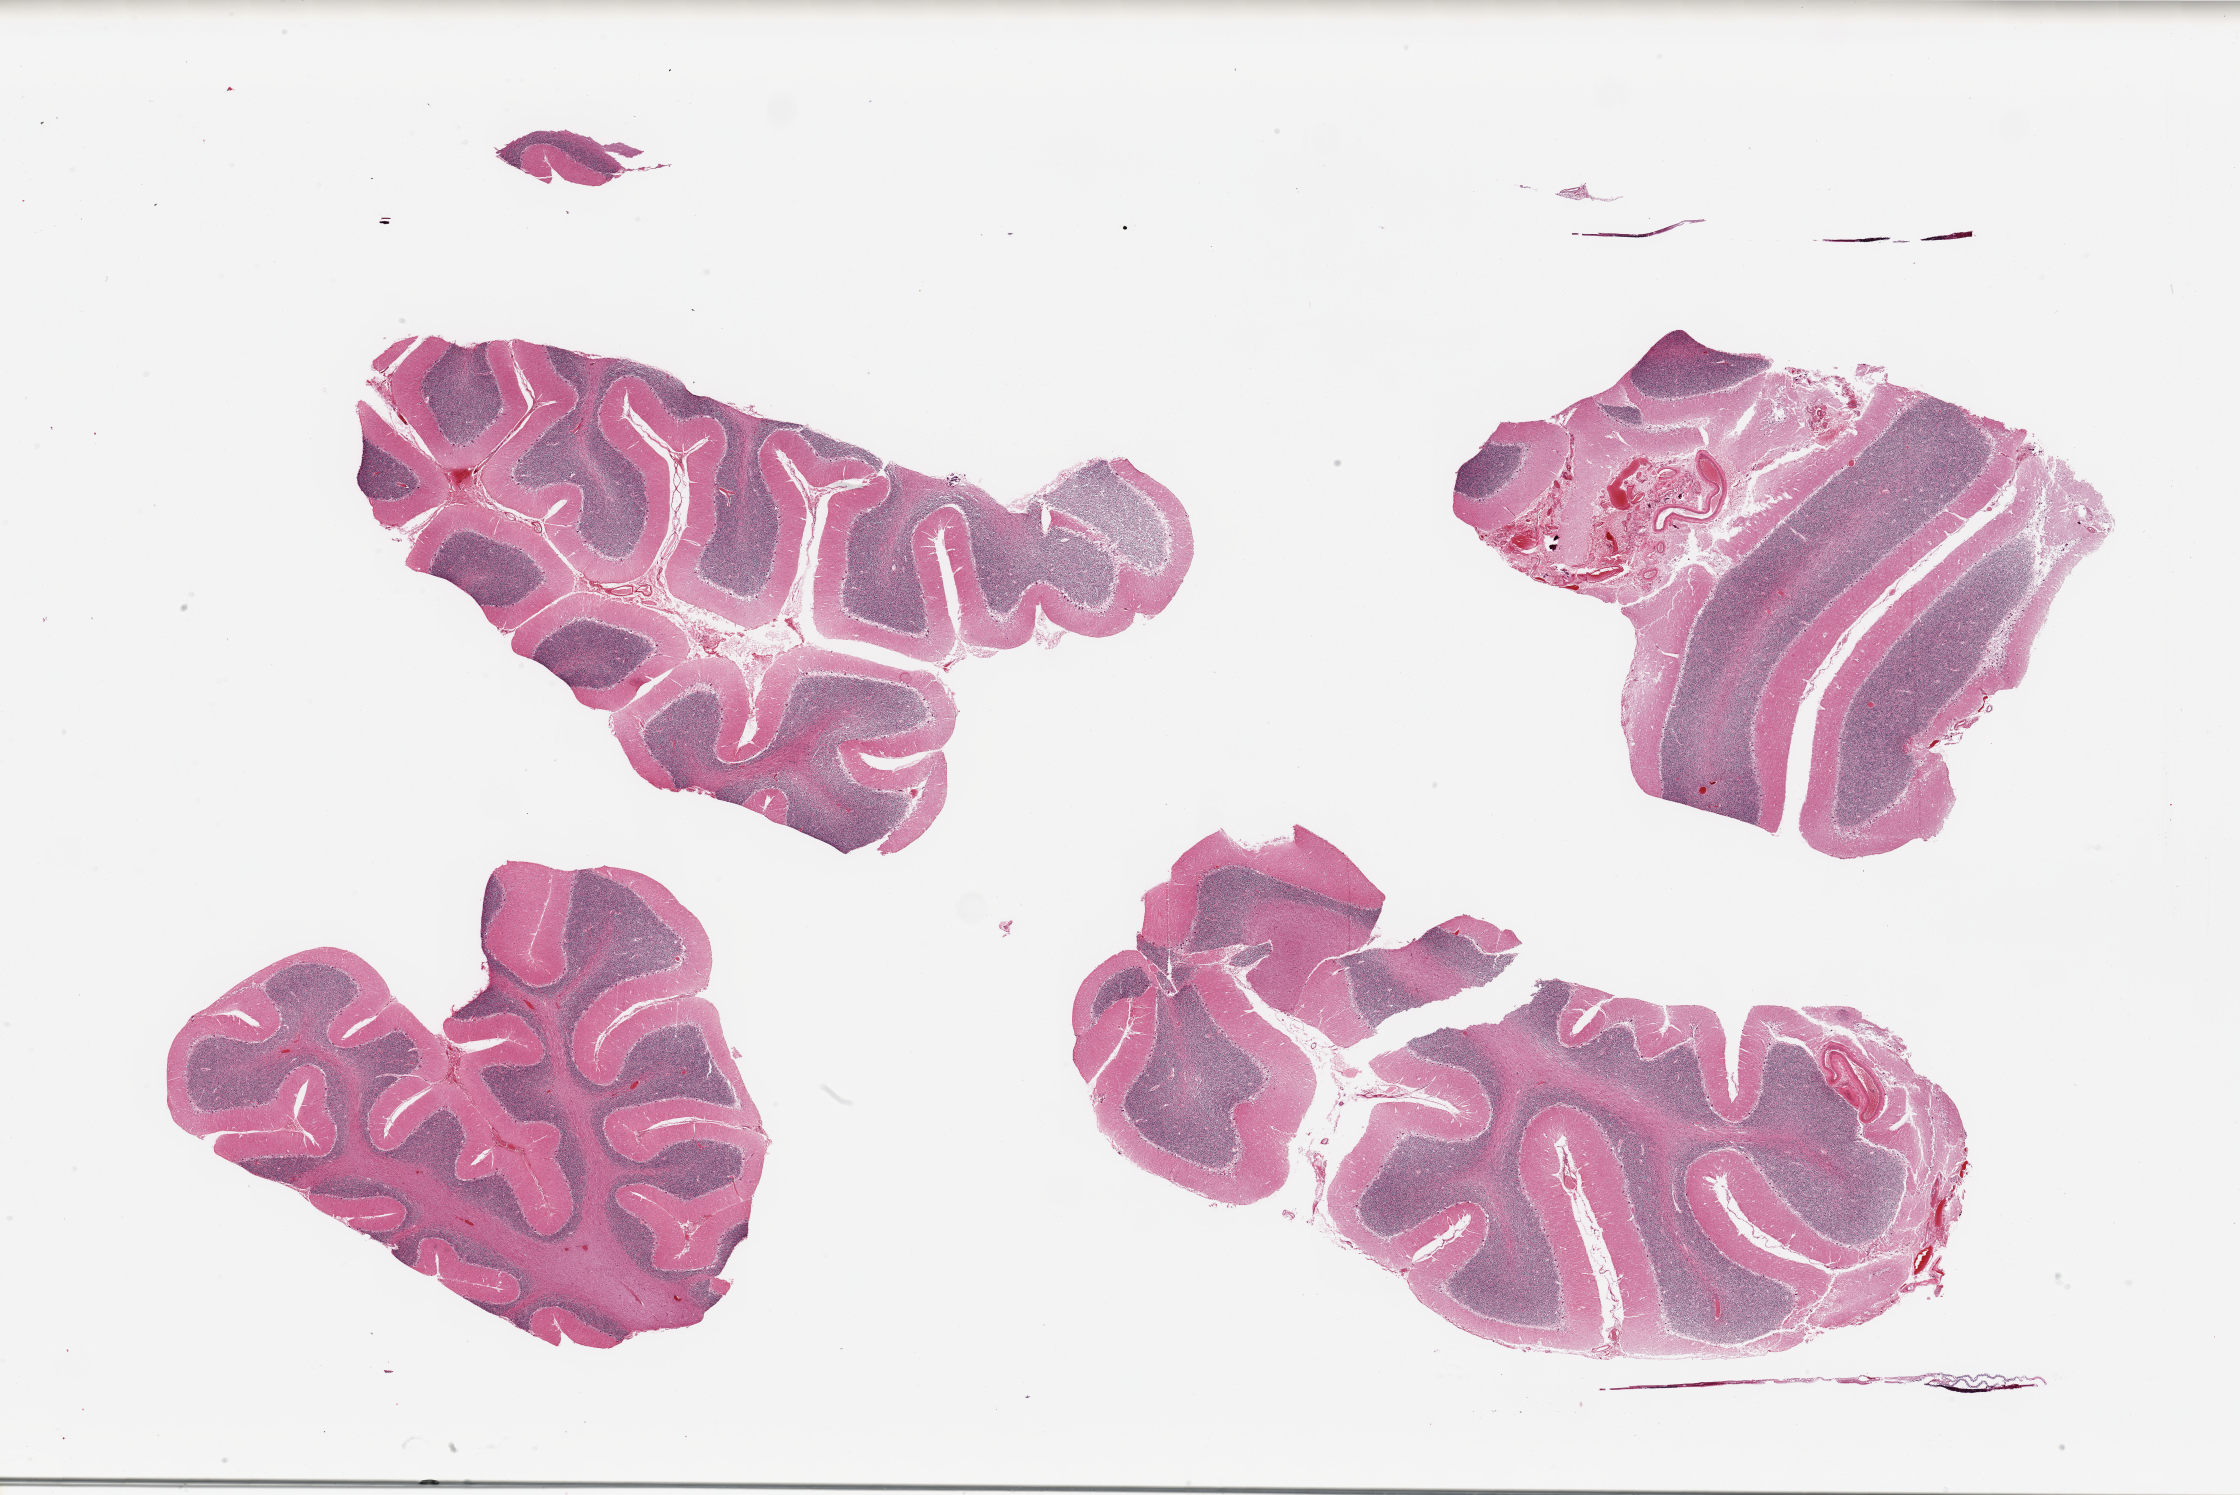
Digitized hematoxylin and eosin (H&E)-stained section — shown as a low-resolution overview of the whole scanned area (about 35.4 x 23.7 mm), PAXgene-fixed paraffin-embedded (PFPE) section, target tissue: cerebellum, donor tissue sample. Donor sex: male.
Reviewer comment on this tissue sample: 4 pieces; 2 of 4 with congested meninges; scattered Purkinje cells present.